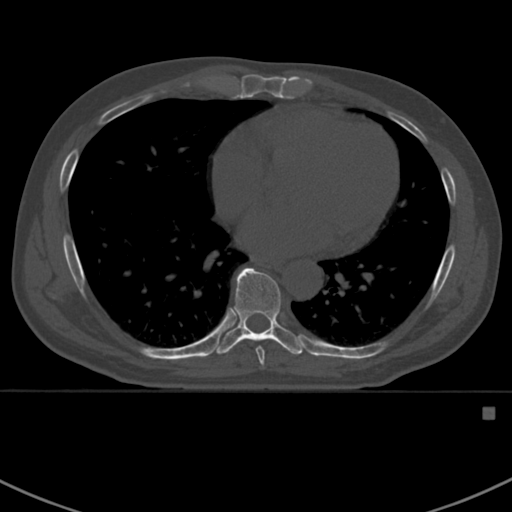
CT including the spine, one axial slice; slice 404 of 412 in the series (ordered by position); reconstruction kernel Br40s; 120 kVp; bone window (W 1800 / L 400 HU); 1.5 mm slice thickness; 512 × 512 image matrix, field of view 358 × 358 mm. Patient: male, 59 years. Case-level facts recorded for this patient, not image findings: primary cancer: prostate.
Outlined on this slice (semi-automatic segmentation, software-assisted and operator-edited):
- T7 vertebra: bounding box (x1, y1, x2, y2) in pixels: (256, 346, 265, 370)
- T8 vertebra: (213, 267, 304, 355)